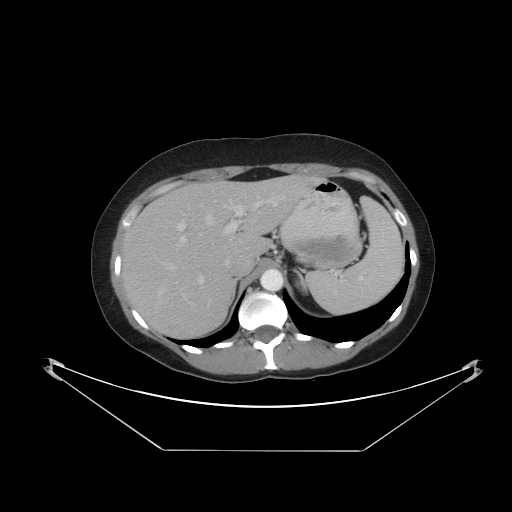
Contrast-enhanced abdominal CT, one axial slice. Slice 32 of 48 in the series (ordered by position). Intravenous contrast given. Soft-tissue window (W 400 / L 40 HU). 5 mm slice thickness. 512 × 512 image matrix, field of view 482 × 482 mm. Female patient, age 38 years. Case-level facts recorded for this patient, not image findings: diagnosis: colorectal cancer liver metastases, imaged before liver resection; multiple liver metastases: yes; largest metastasis: 2.5 cm; disease in both lobes: no.
Structures marked on this image (manually delineated by an expert):
- hepatic veins: bounding box [x1, y1, x2, y2] px = [159, 193, 246, 294]
- liver: [120, 176, 320, 339]
- planned liver remnant (the part of the liver to remain after resection): [178, 176, 304, 256]
- portal vein (with intrahepatic branches): [177, 196, 285, 284]
- liver metastasis: [304, 179, 314, 189]